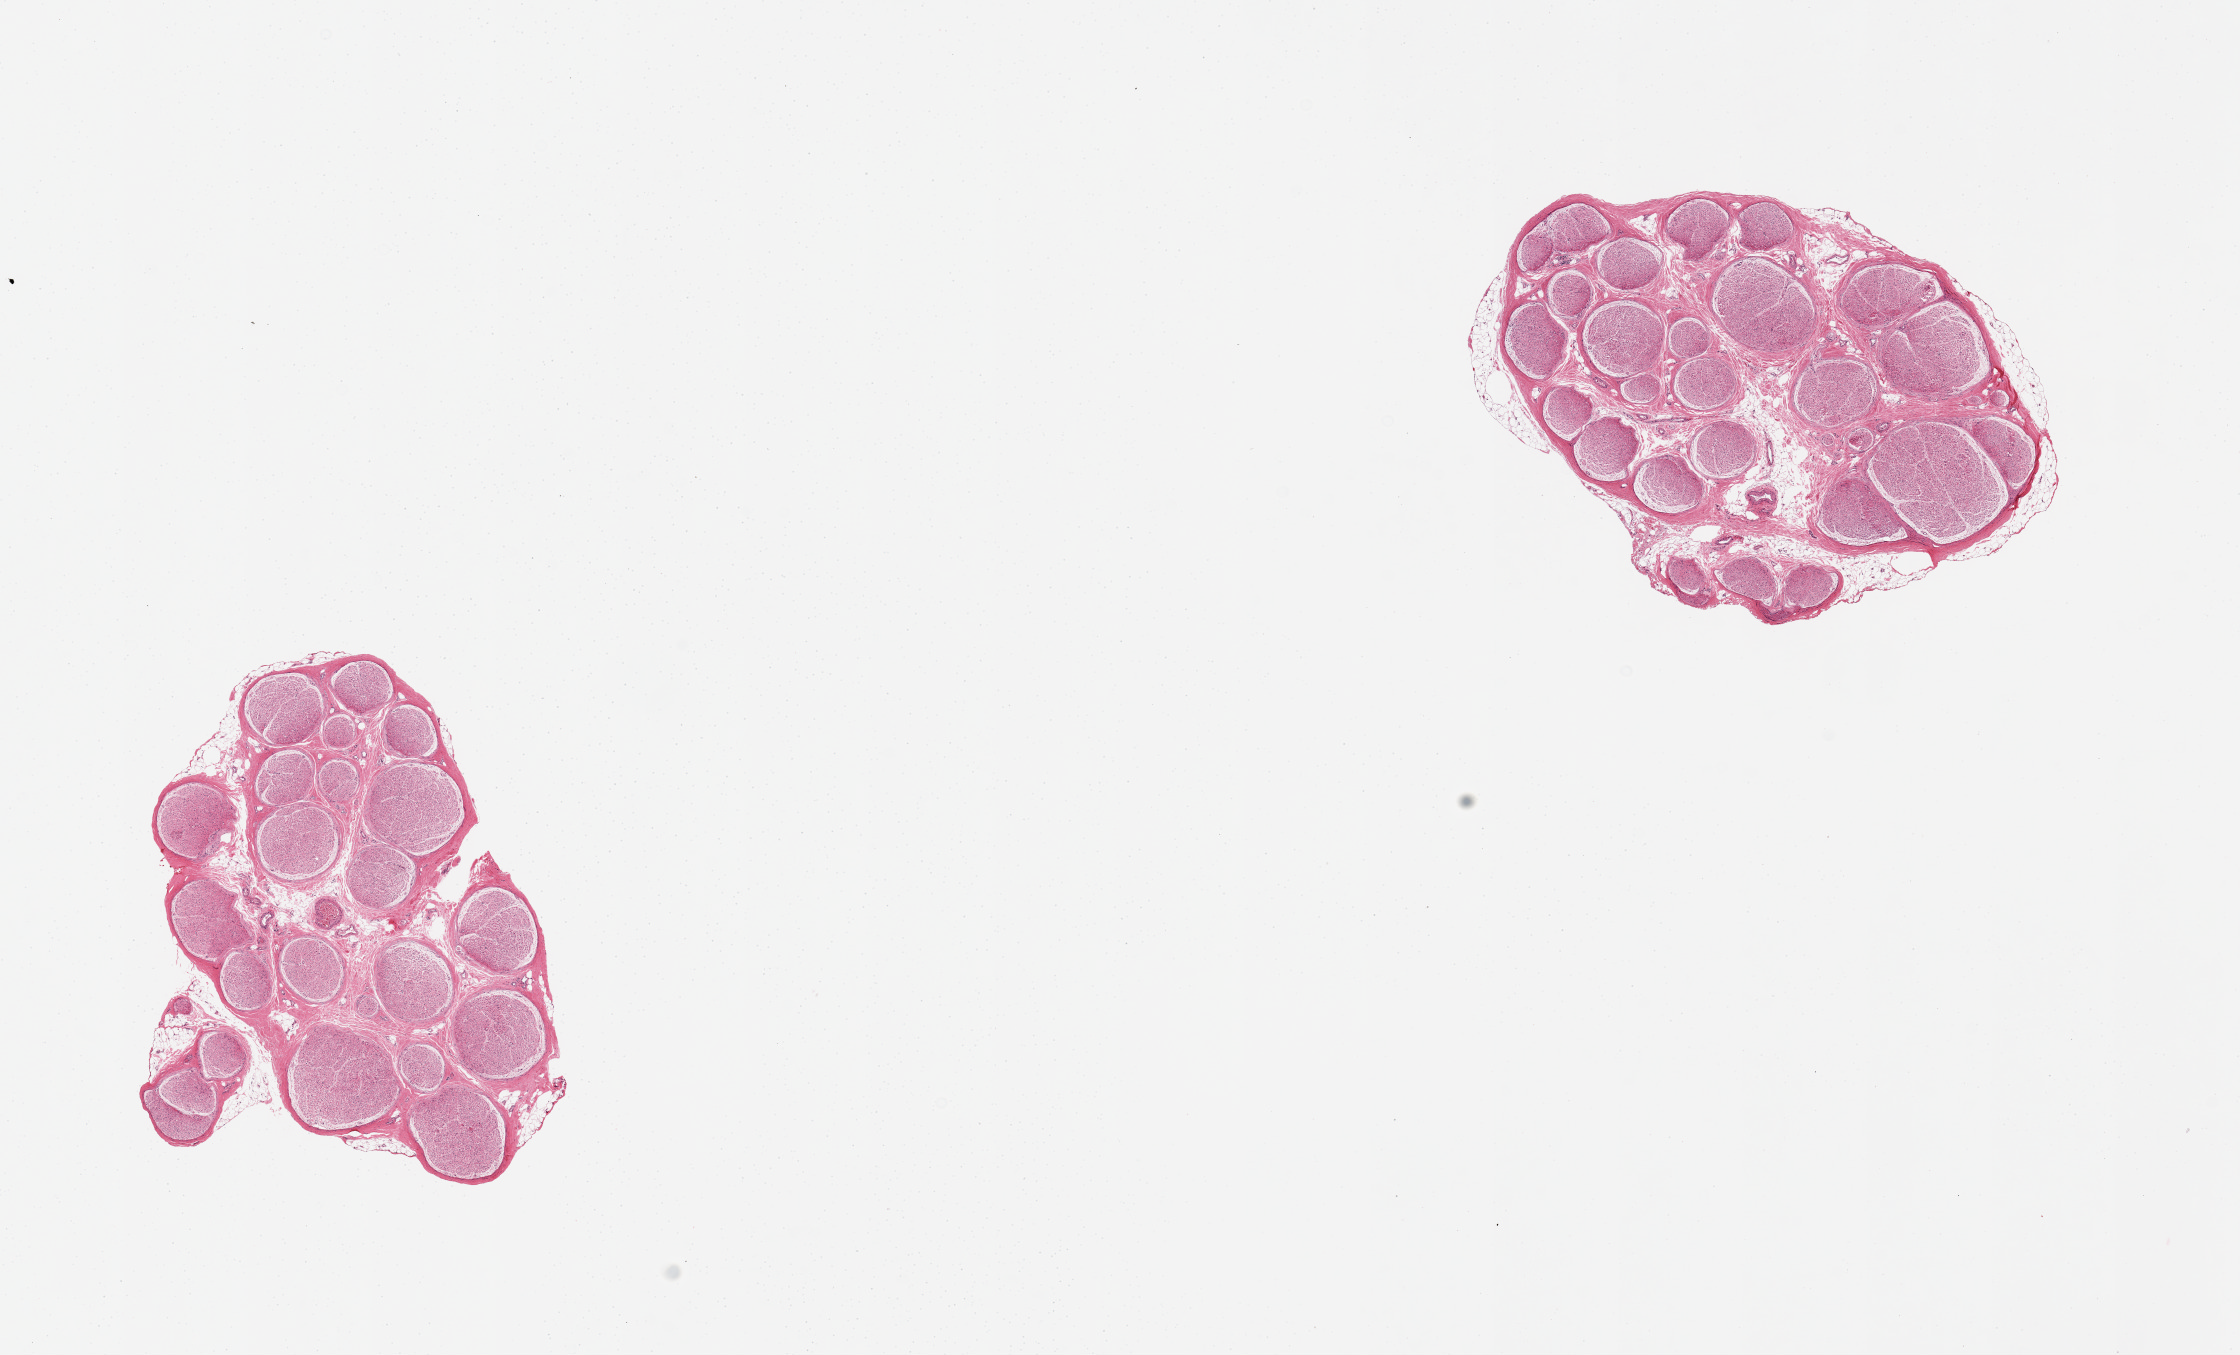
Haematoxylin and eosin whole-slide image — a low-resolution overview of the entire scanned area, about 17.7 x 10.7 mm (slide scanned at 20x). Donor sex: female.
Specimen: PAXgene-fixed paraffin-embedded (PFPE) section; target tissue: tibial nerve; donor tissue sample.